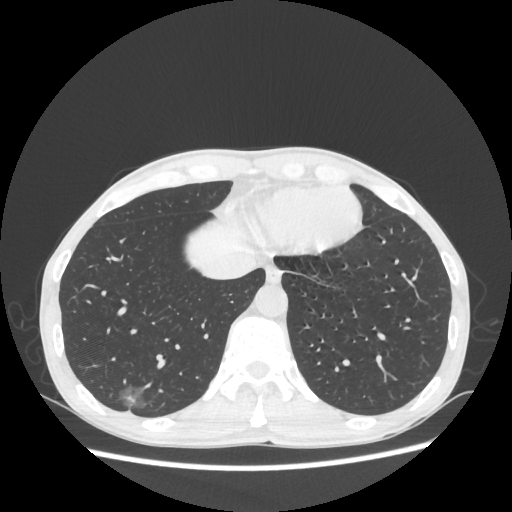
Chest CT, one axial slice; position 69 of 270 along the scan axis; reconstruction kernel STANDARD; lung window (W 1500 / L -600 HU); 512 × 512 image matrix. Patient: male, 60 years. From the clinical record (not read from this slice): clinical TNM (as recorded): T1c N0 M0; histopathological grade: G2.
Outlined on this slice (rectangle marked by the reading radiologist):
- lung tumour (recorded histology: adenocarcinoma): bounding box [x1, y1, x2, y2] px = [112, 380, 148, 409]